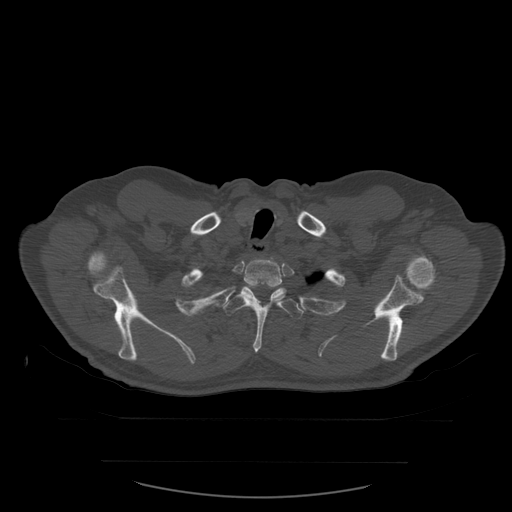
CT including the spine, one axial slice; position 467 of 590 along the scan axis; bone window (W 1800 / L 400 HU); 1.25 mm slice thickness; 512 × 512 image matrix, field of view 479 × 479 mm. Patient age 71 years. From the clinical record (not read from this slice): primary cancer: lung.
Structures marked on this image (semi-automatic segmentation, software-assisted and operator-edited):
- T2 vertebra: bounding box <243,258,283,293> (left, top, right, bottom; pixels)
- T3 vertebra: <223,288,304,353>